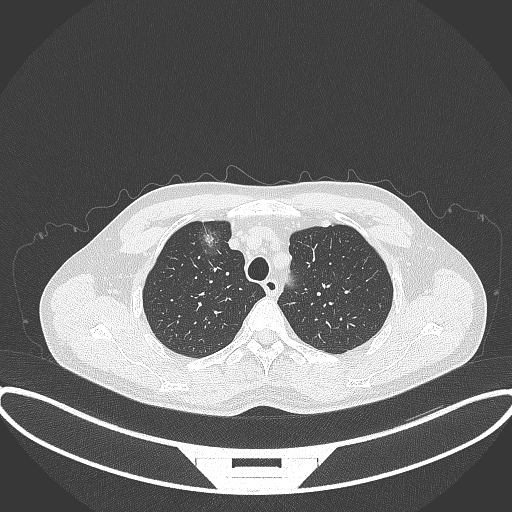
Chest CT, one axial slice. Reconstruction kernel B70f. 120 kVp. Lung window (W 1500 / L -600 HU). 1 mm slice thickness. 512 × 512 image matrix, field of view 424 × 424 mm. Patient: male, 60 years. Case-level facts recorded for this patient, not image findings: clinical TNM (as recorded): T1c N0 M0.
Annotated regions visible in this slice (rectangle marked by the reading radiologist):
- lung tumour (recorded histology: adenocarcinoma): bounding box <194,211,231,261> (left, top, right, bottom; pixels)